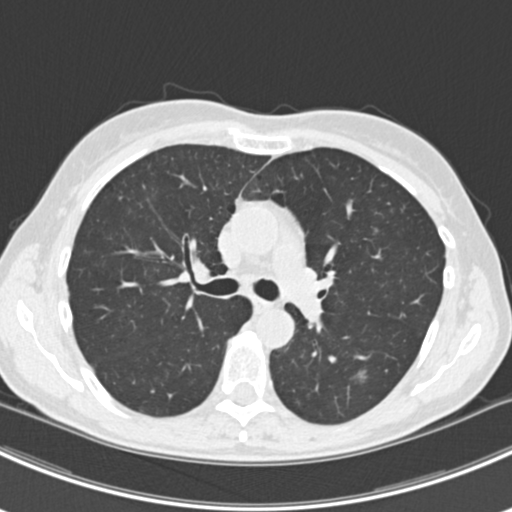
Low-dose screening chest CT, axial slice. Baseline annual screen. Lung window (W 1500 / L -600 HU). Slice 70 of 224 in the series. Female participant, aged 63 years at enrolment.
Expert-annotated lung lesion, bounding box [x1, y1, x2, y2] px = [343, 362, 380, 392]. The screening reader recorded 10 non-calcified nodules or masses ≥4 mm on this exam (right lower lobe, right lower lobe, left lower lobe, left lower lobe, right middle lobe, right lower lobe, left lower lobe, left upper lobe, right upper lobe, left upper lobe); which of them this box marks is not recorded. Lung cancer was diagnosed 751 days after this screen: bronchiolo-alveolar adenocarcinoma, NOS, right upper lobe, right middle lobe, right lower lobe, left upper lobe, left lower lobe, moderately differentiated (G2), stage IV (AJCC 6th edition).